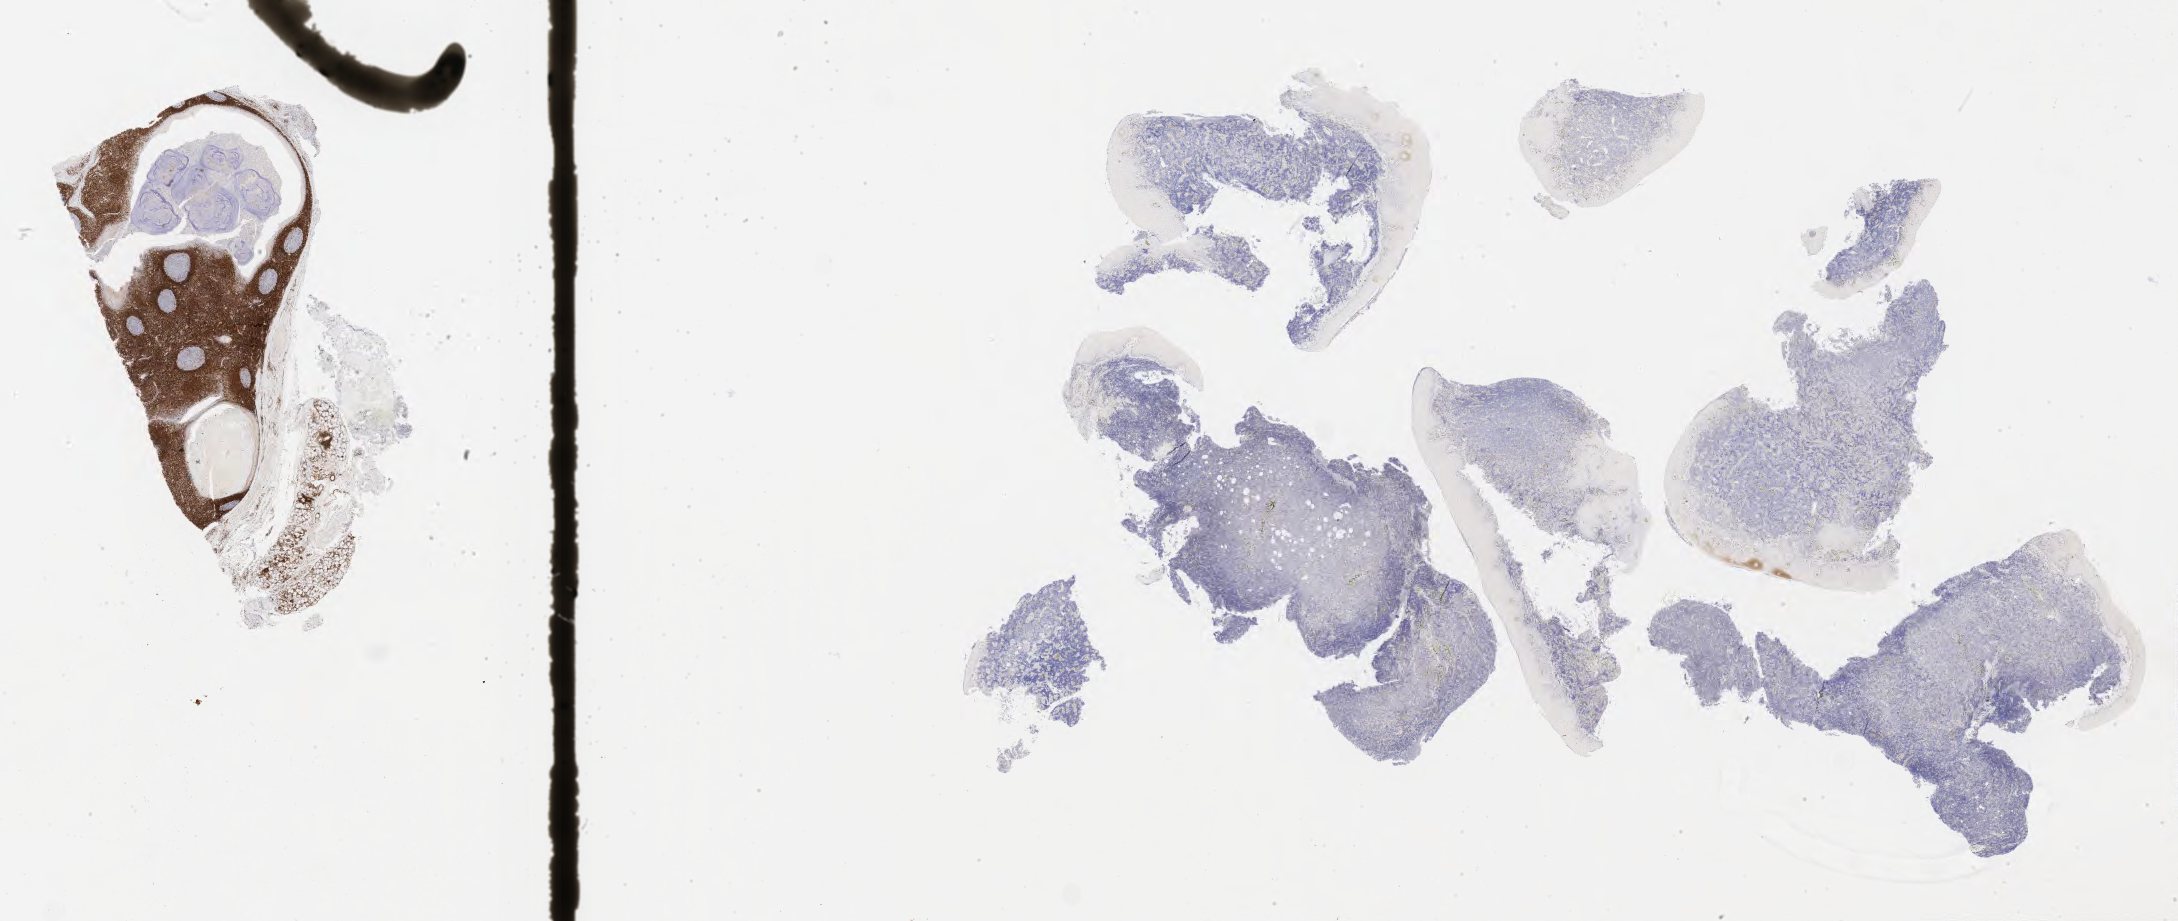
Immunohistochemistry (IHC) whole-slide image stained for BCL2, a low-resolution overview of the entire scanned area, about 35.2 x 14.9 mm, specimen: tumor tissue. Patient male; 43 years old.
• histologic diagnosis: Burkitt lymphoma, NOS